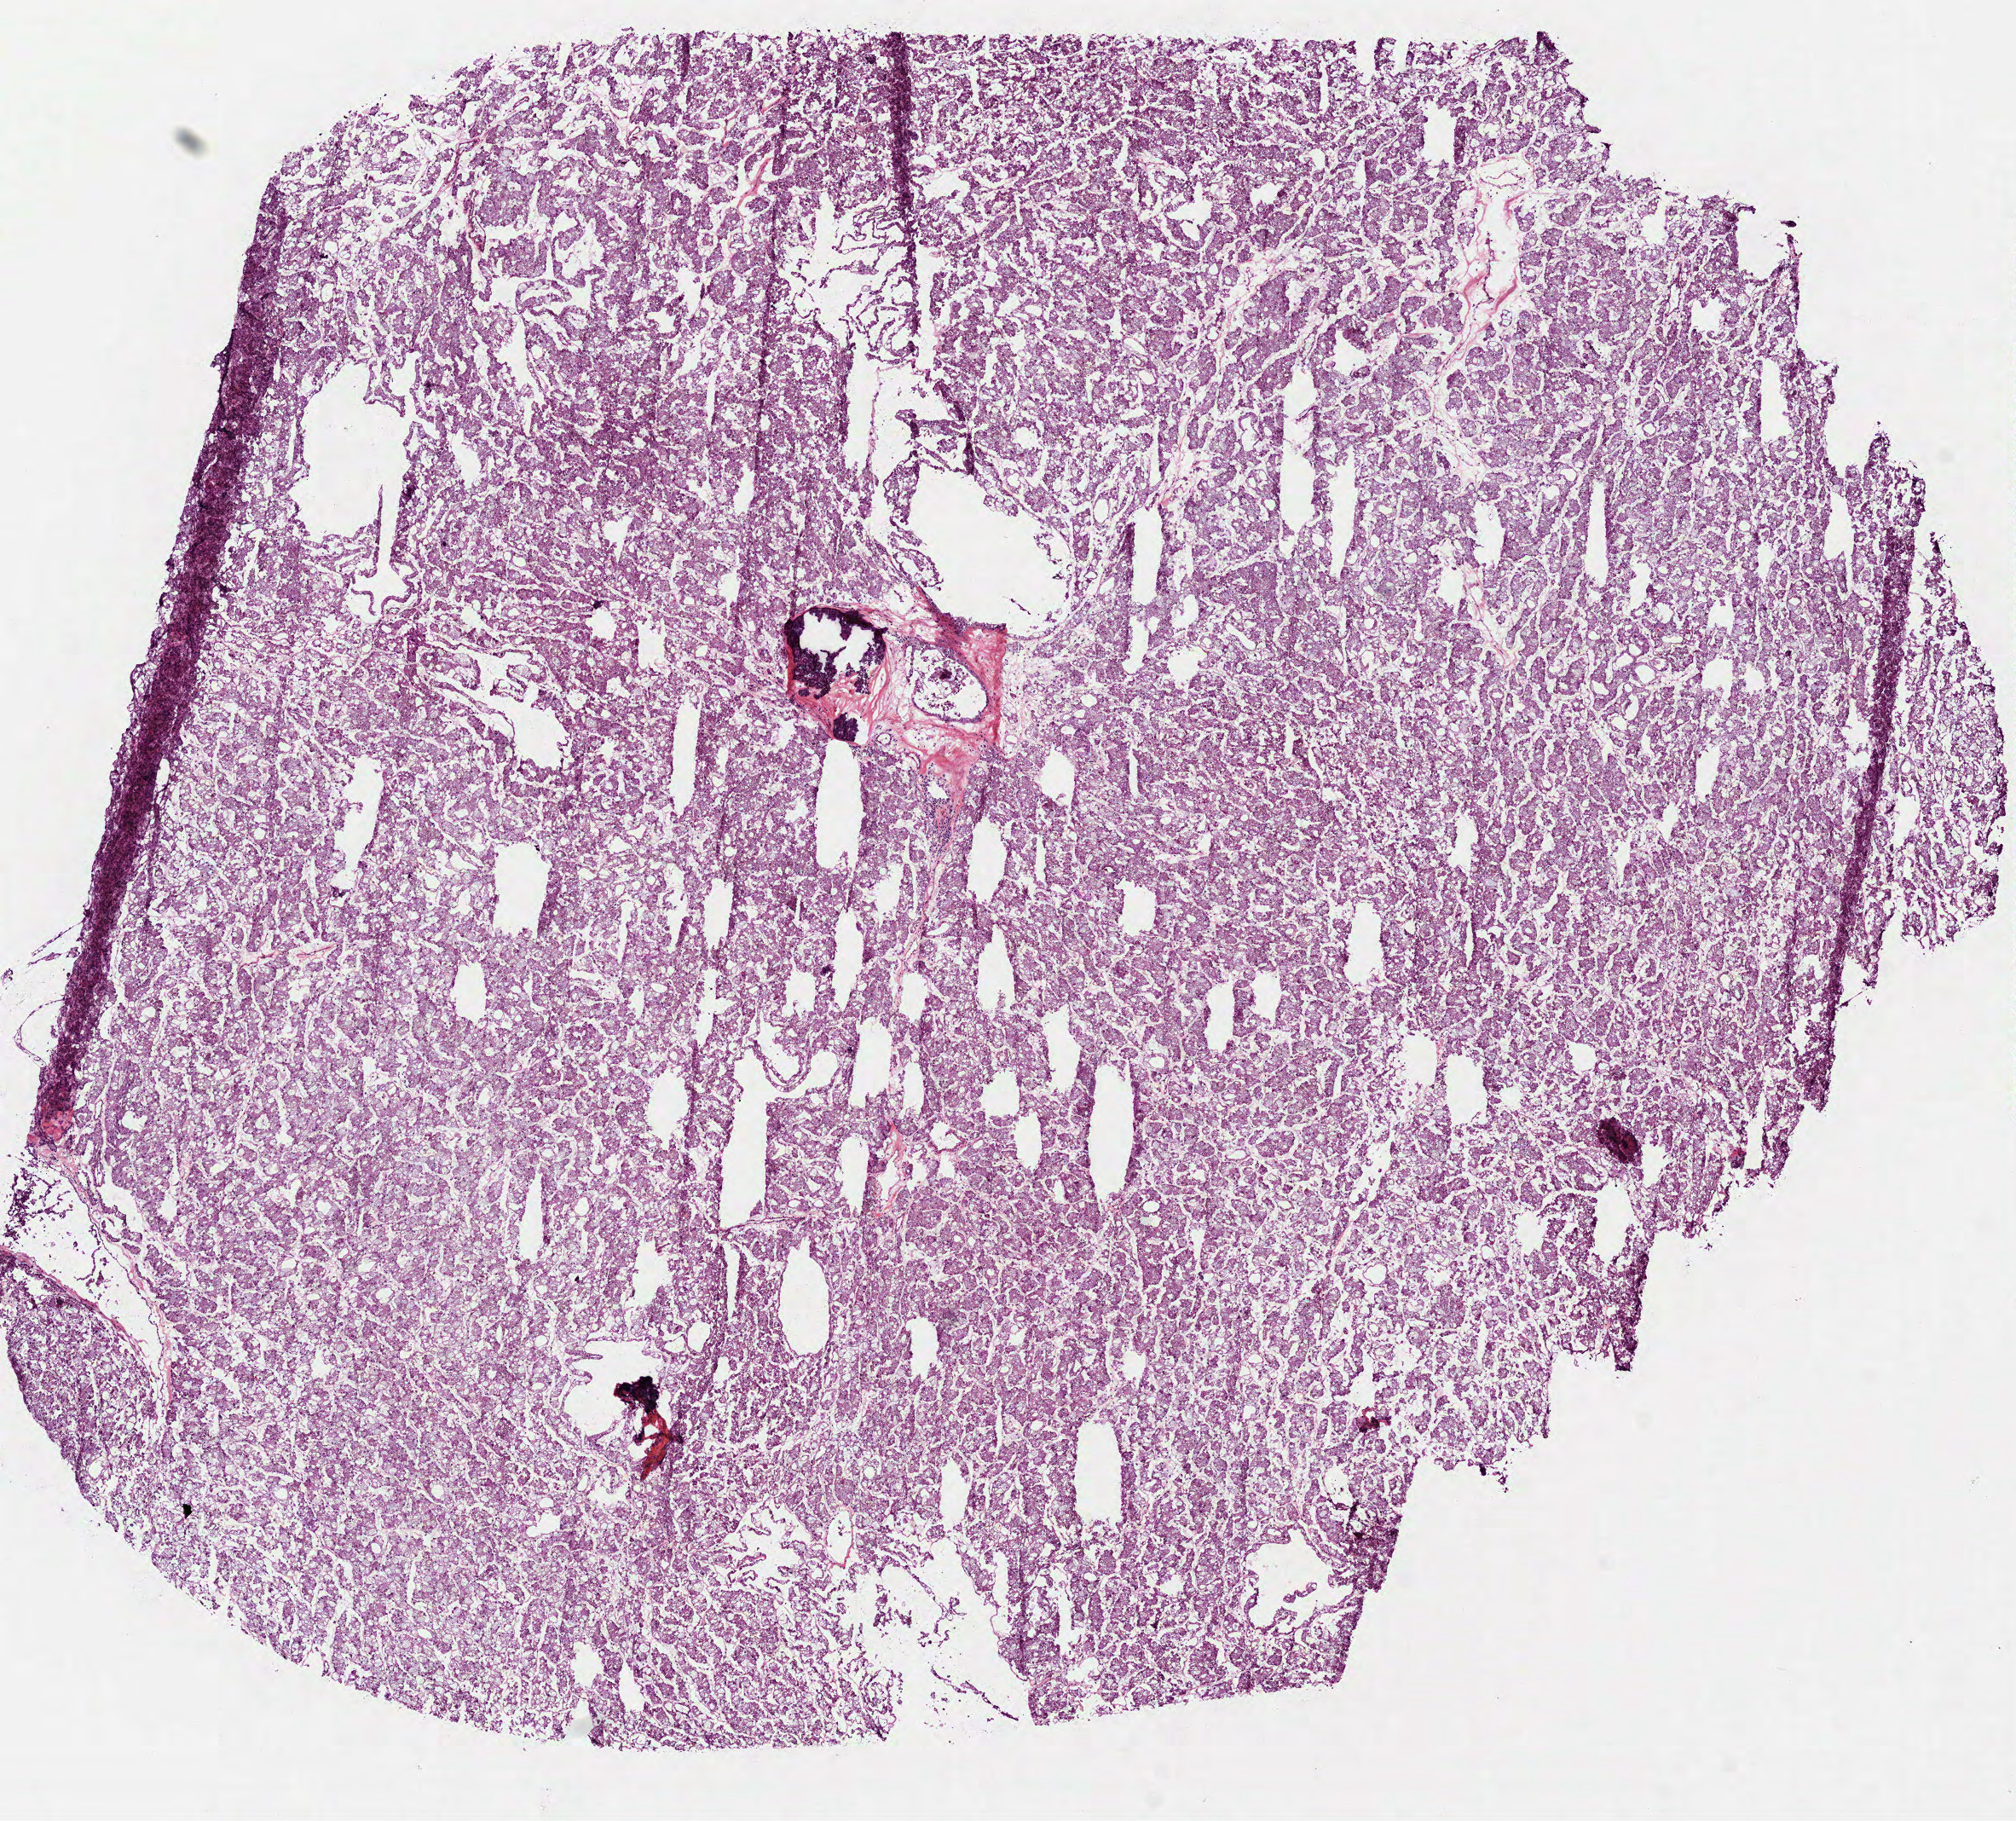
H&E whole-slide image, a low-resolution overview of the entire scanned area, about 9.5 x 8.6 mm. Frozen section. Primary tumour sample from the kidney. Female, age 66 years at initial diagnosis. Slide review estimates, as recorded: tumour cells 100%, tumour nuclei 80%.
Diagnosis: Renal cell carcinoma, chromophobe type.